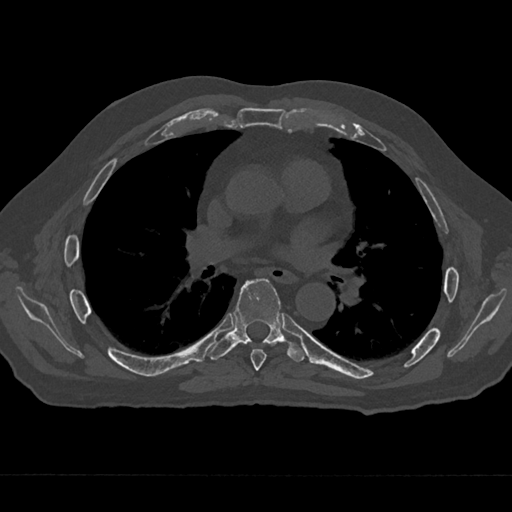
CT including the spine, one axial slice; slice 393 of 797 in the series (ordered by position); bone window (W 1800 / L 400 HU); 0.5 mm slice thickness; 512 × 512 image matrix, field of view 377 × 377 mm. Patient: male, 75 years. Case-level facts recorded for this patient, not image findings: primary cancer: renal; vertebrae with lytic lesions (as recorded): T4.
Structures marked on this image (semi-automatic segmentation, software-assisted and operator-edited):
- T6 vertebra: bounding box (x1, y1, x2, y2) in pixels: (250, 344, 276, 371)
- T7 vertebra: (208, 278, 305, 362)